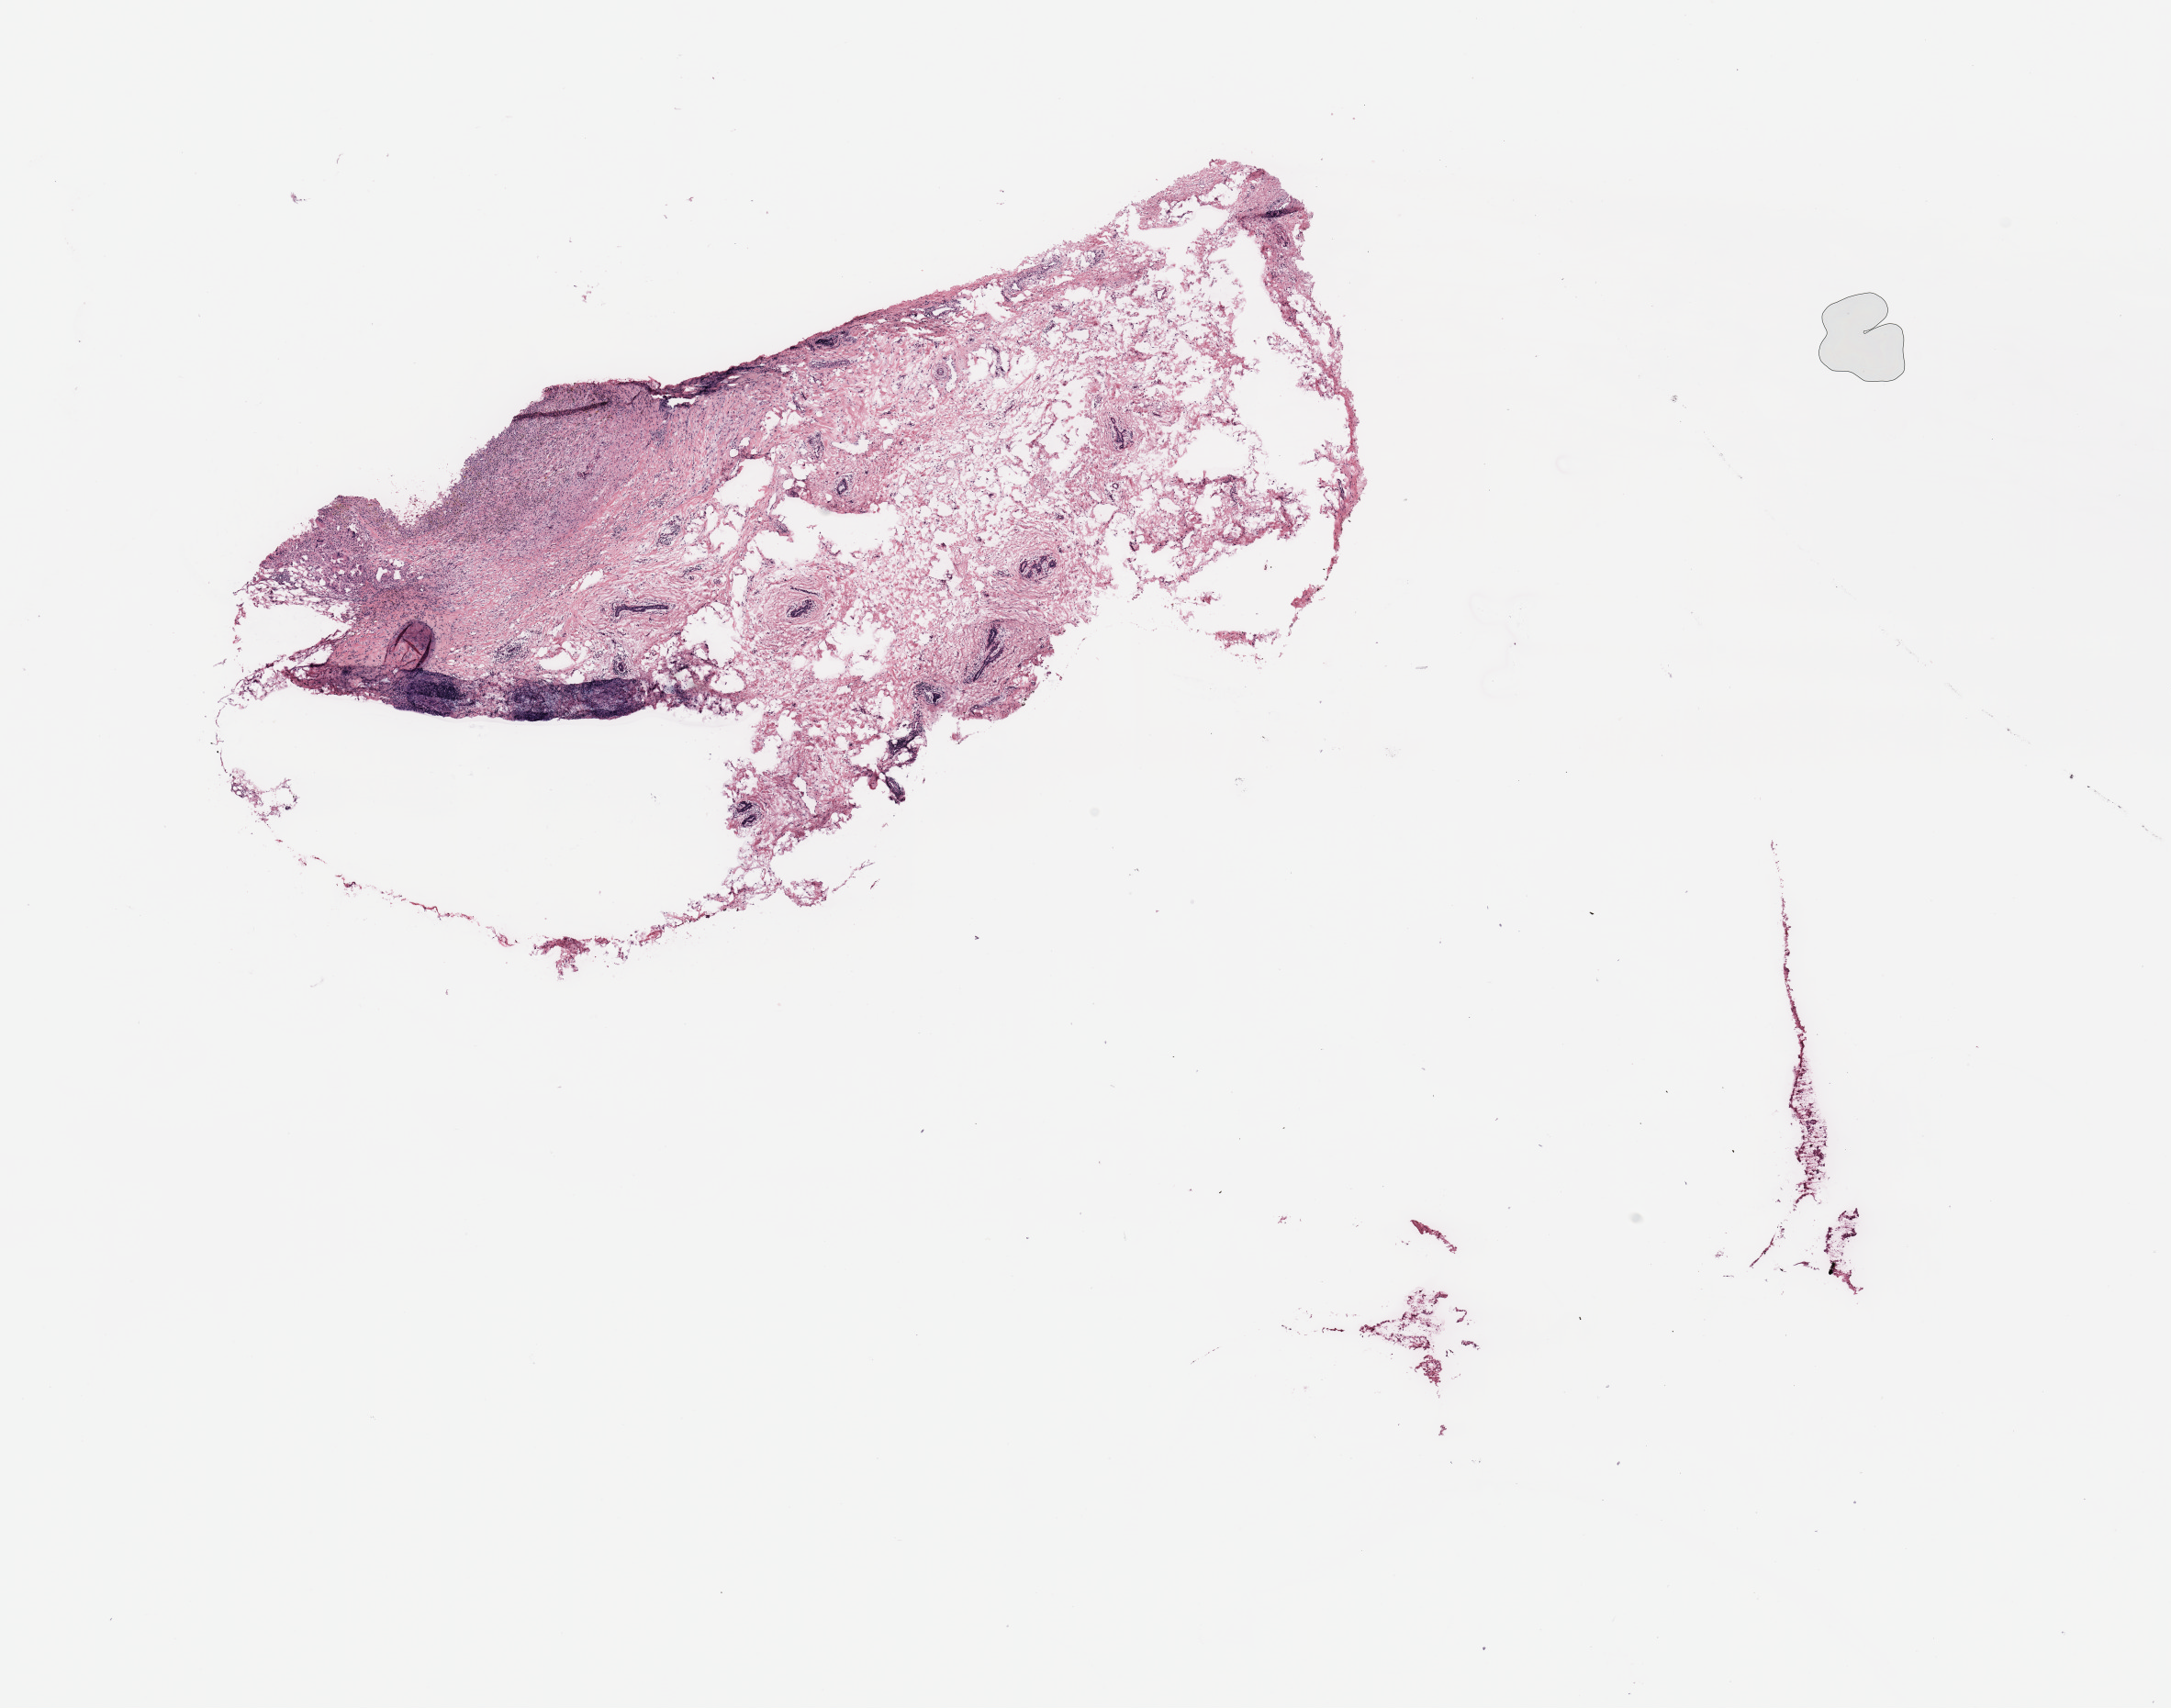
Whole-slide histology image, H&E-stained, low-resolution overview of the scanned area, about 18.7 x 14.7 mm; breast, tissue type not recorded.
• patient diagnosis (cohort enrolment): breast cancer (breast)